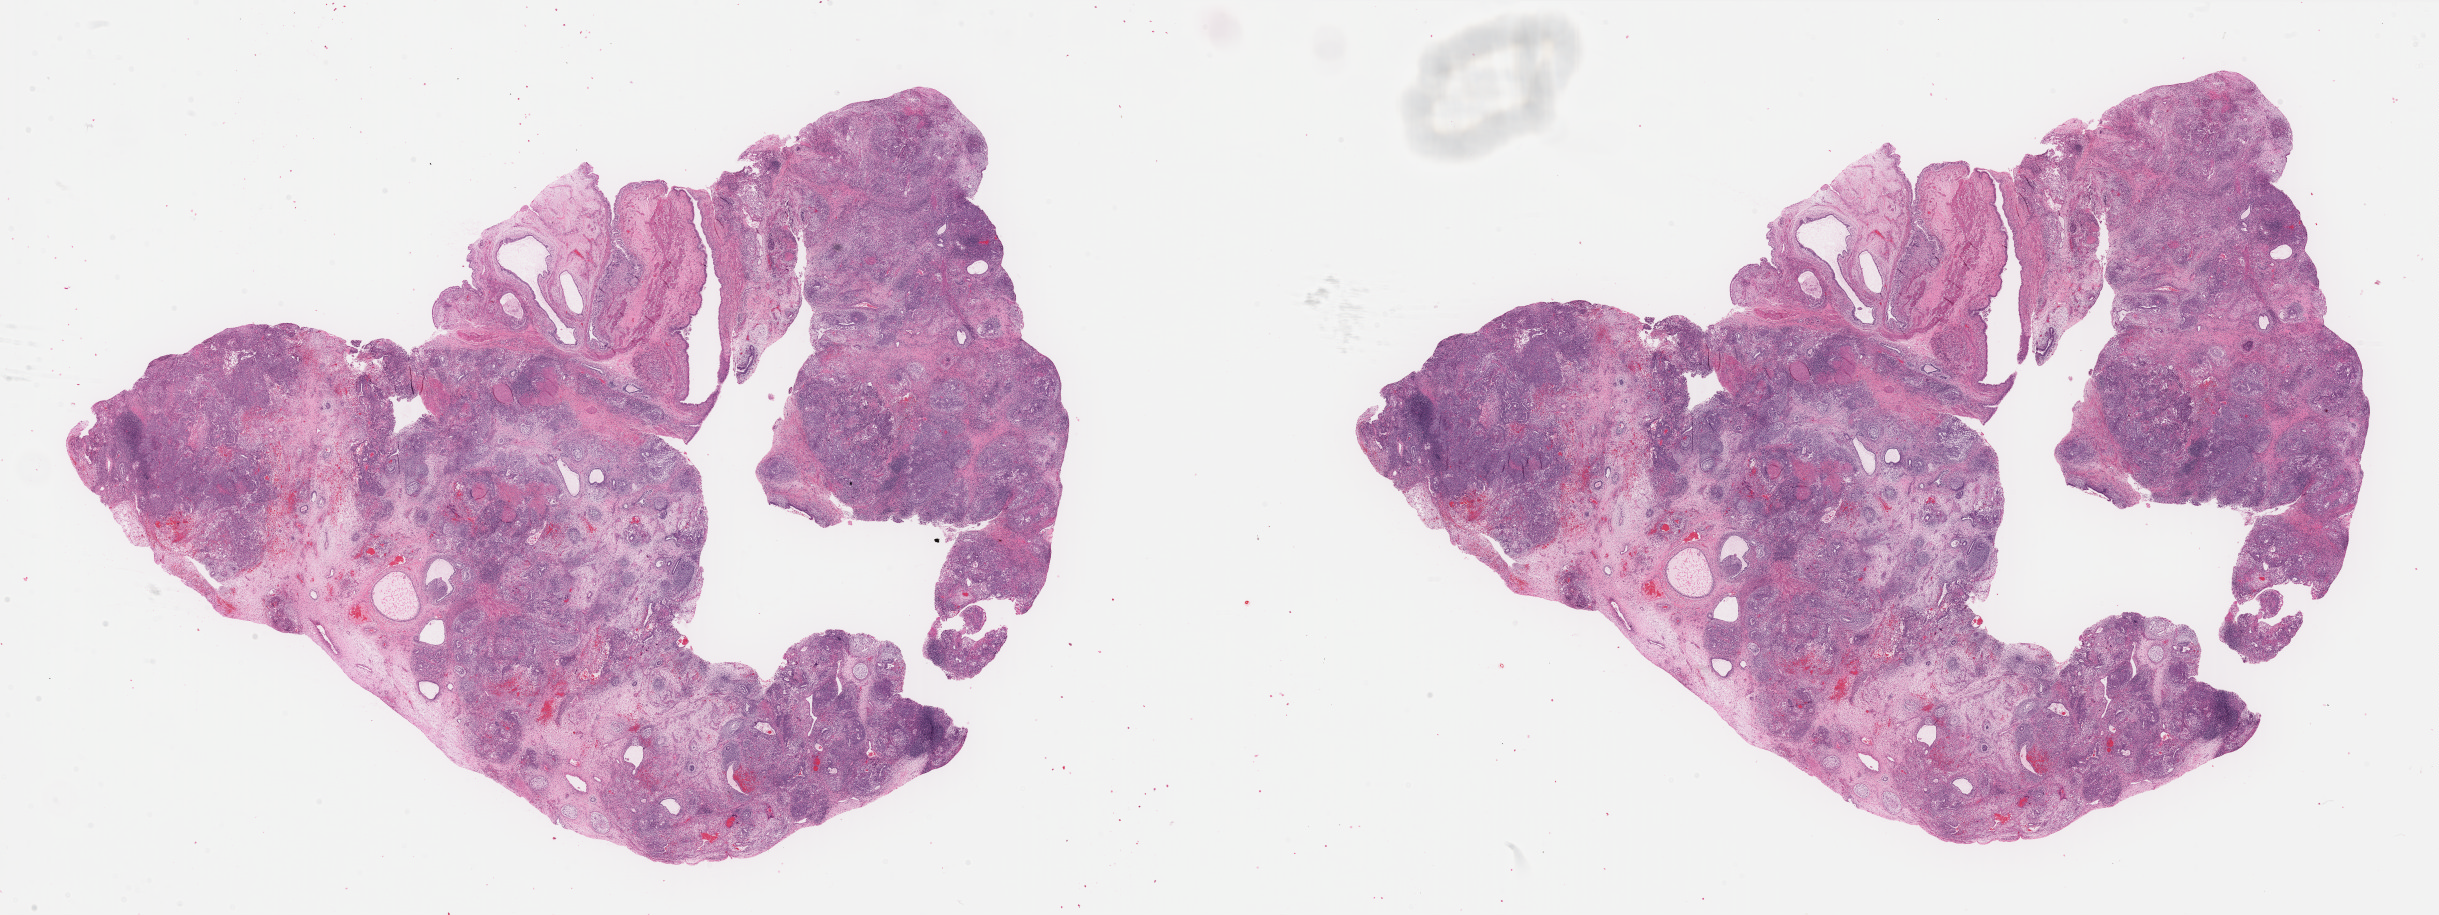
Digitized H&E tissue section (whole slide) — low-resolution overview of the scanned area, about 38.6 x 14.5 mm (slide scanned at 40x). Formalin-fixed paraffin-embedded (FFPE) diagnostic section. Sample: primary tumour, testis. Male patient; age at initial diagnosis 26 years.
Pathologic diagnosis: Mixed germ cell tumor.